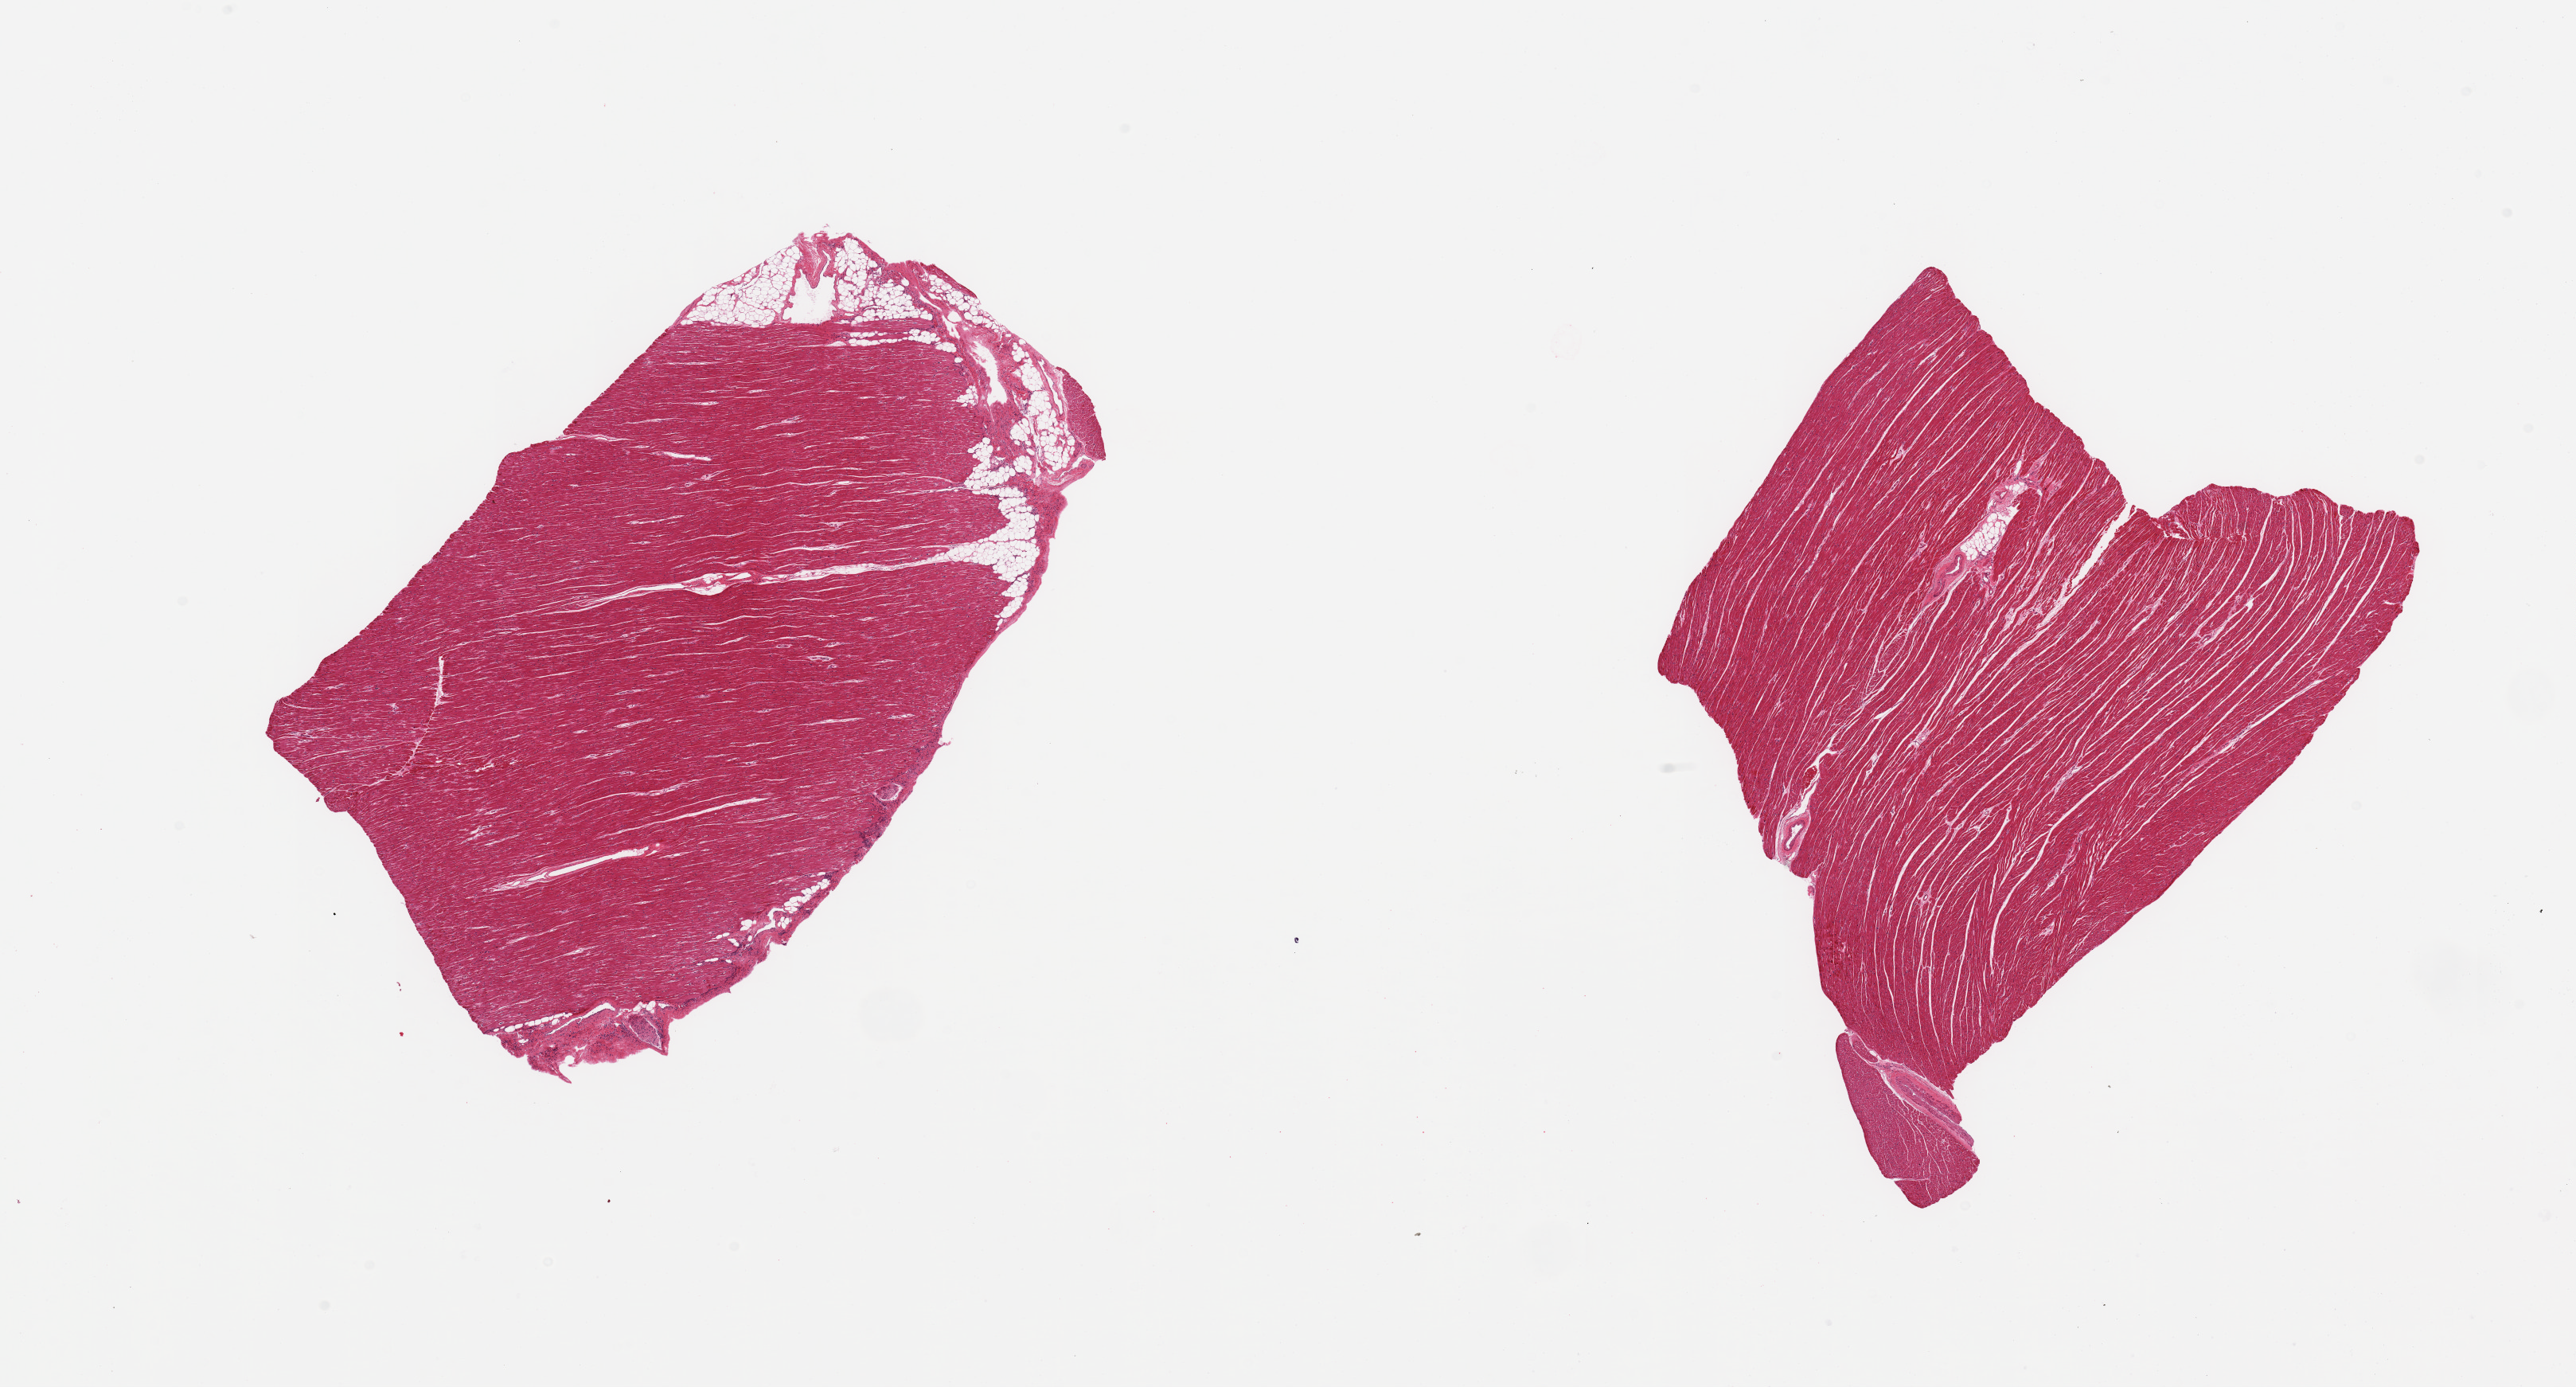
H&E whole-slide image — low-resolution overview of the scanned area, about 25.6 x 13.8 mm. PAXgene-fixed paraffin-embedded (PFPE) section. Sampled site (target tissue): heart. Donor tissue sample. Female donor.
Reviewer comment on this tissue sample: 2 pieces, mild interstitial fibrosis; ~10% epicardial fat.